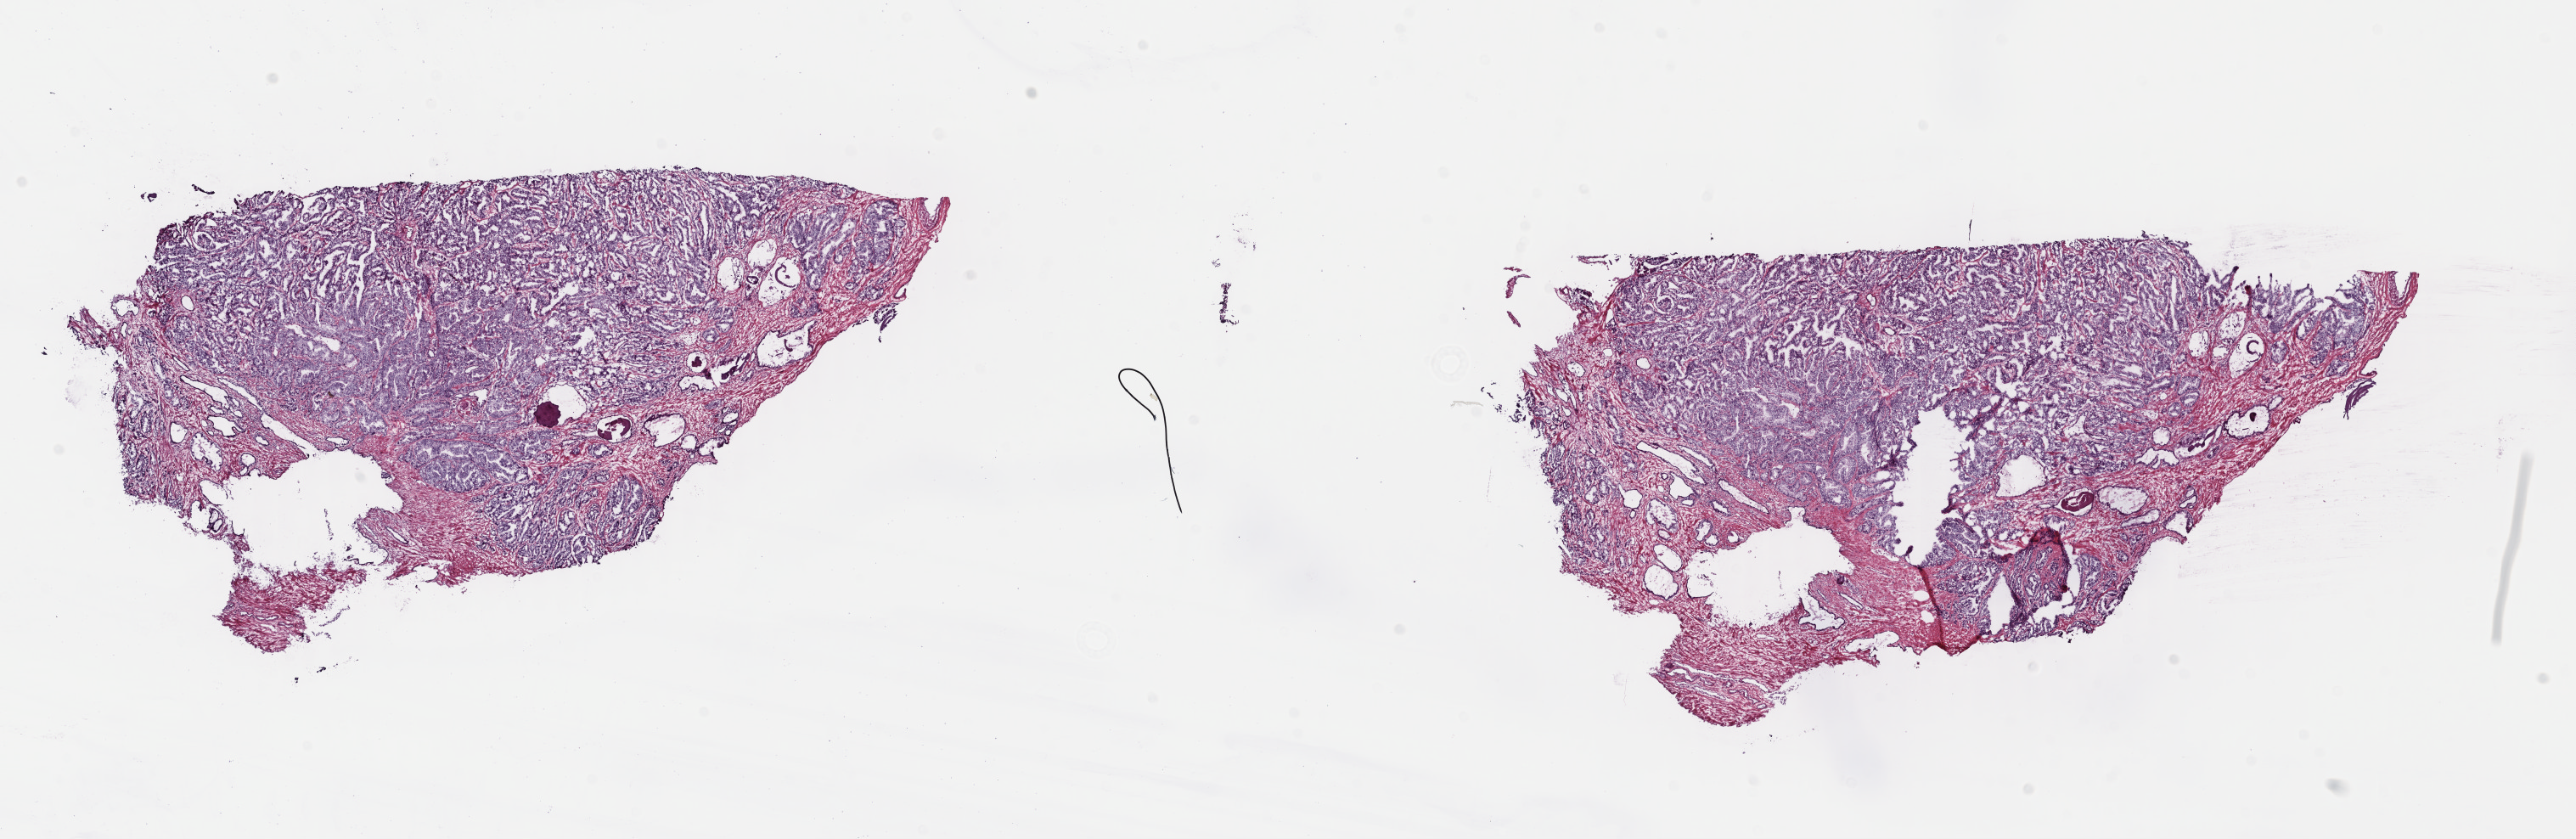
Whole-slide histology image, Hematoxylin and eosin (H&E) stained — a low-resolution overview of the entire scanned area, about 23.8 x 7.8 mm. Frozen section. Prostate, primary tumour sample. Male, age 66 years at initial diagnosis. Gleason score: 7 (4+3). Slide review estimates, as recorded: tumour cells 75%, tumour nuclei 80%, normal cells 3%, stromal cells 22%, necrosis 0%. Infiltration values recorded for this section: lymphocyte infiltration 0%, monocyte infiltration 0%, neutrophil infiltration 0%.
* histologic diagnosis: Adenocarcinoma, NOS (prostate gland)
* lymph nodes positive (case pathology): 0 of 2 examined